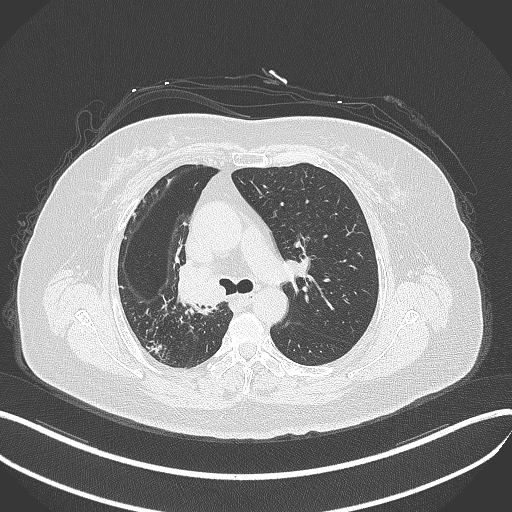
Chest CT, one axial slice. Position 234 of 376 along the scan axis. Reconstruction kernel B70f. 120 kVp. Lung window (W 1500 / L -600 HU). 1 mm slice thickness. 512 × 512 image matrix, field of view 400 × 400 mm. Patient: female, 60 years. From the clinical record (not read from this slice): clinical TNM (as recorded): T1c N0 M0.
Structures marked on this image (rectangle marked by the reading radiologist):
- lung tumour (recorded histology: squamous cell carcinoma): bounding box [x1, y1, x2, y2] px = [170, 261, 233, 308]